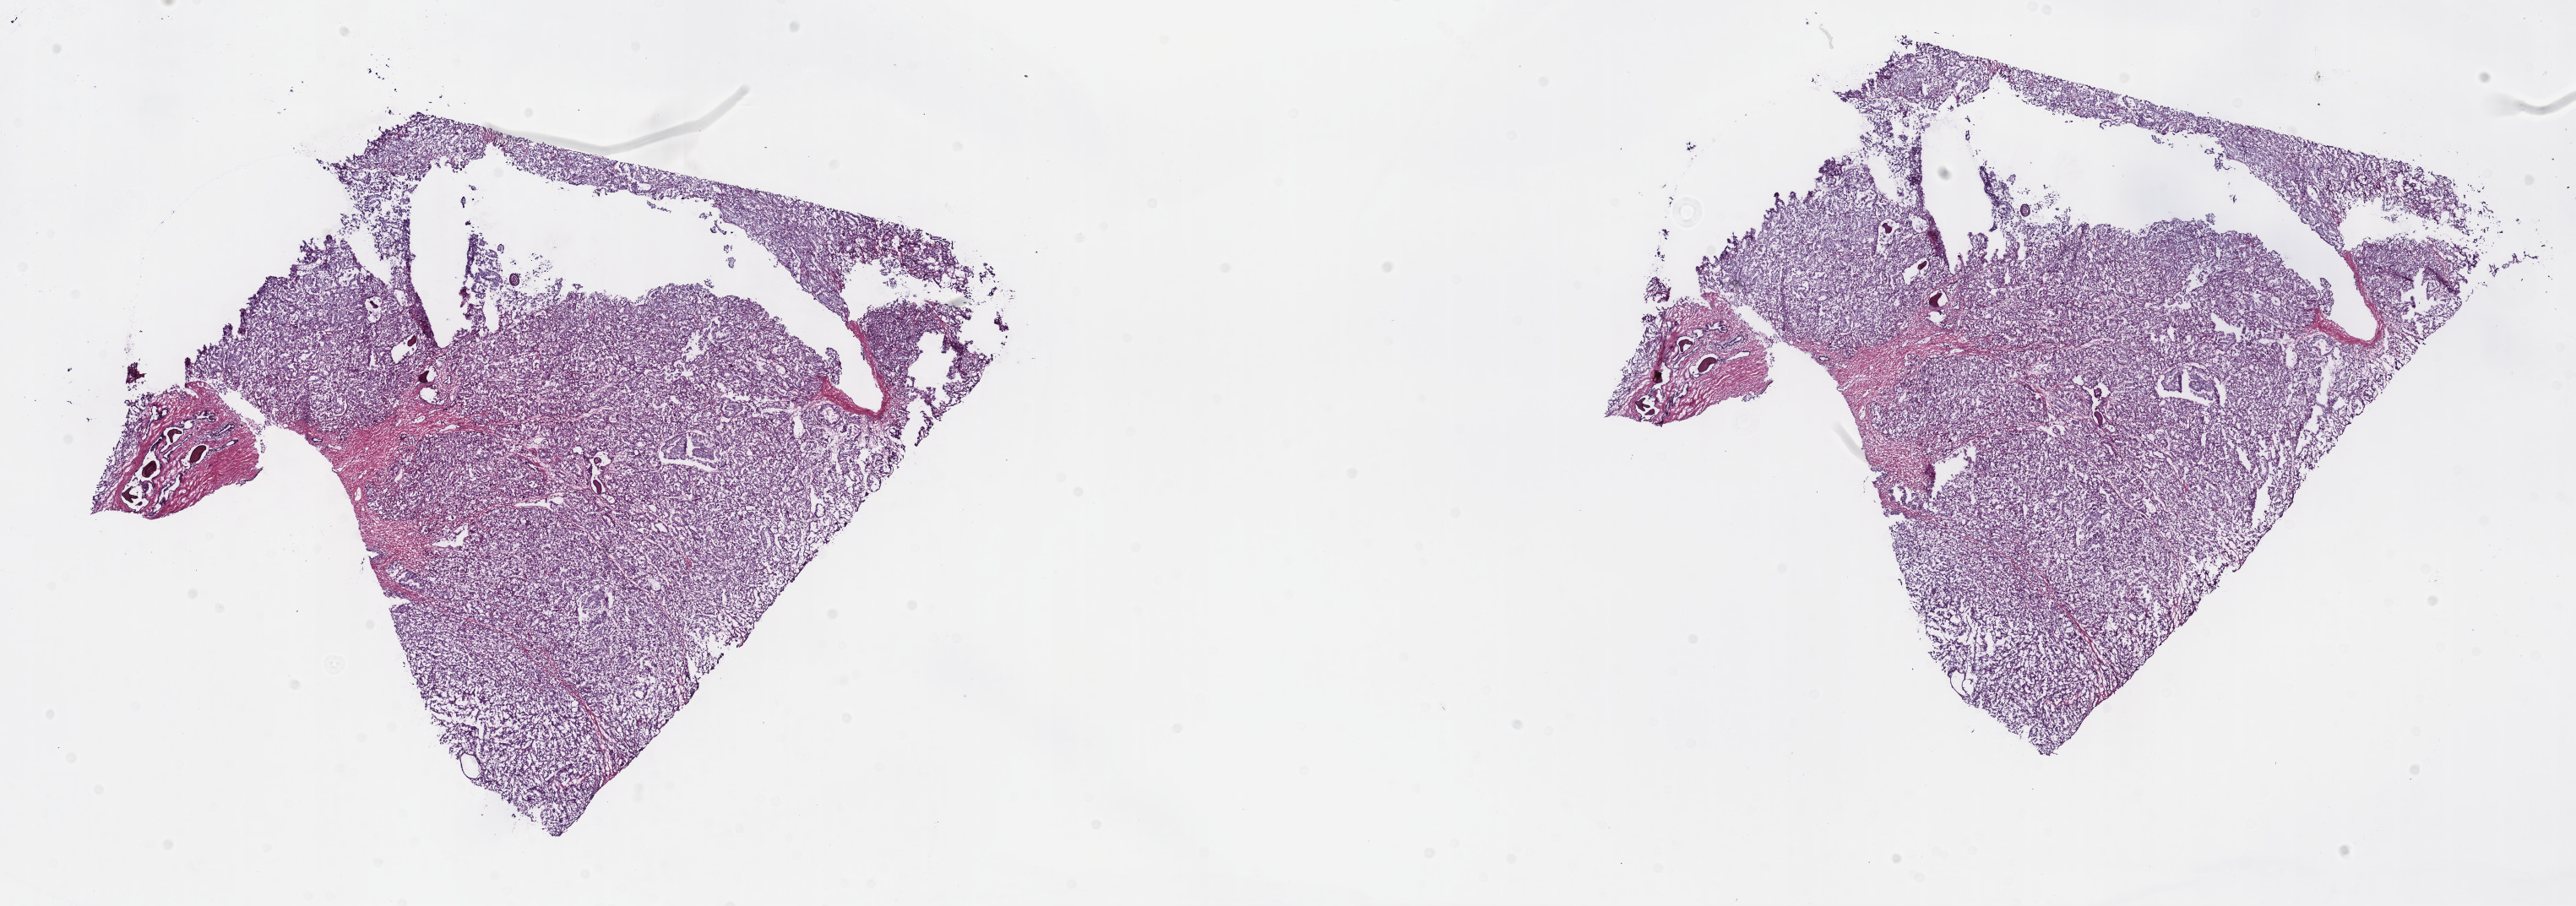
Whole-slide histology image, H&E-stained, a low-resolution overview of the entire scanned area, about 24.7 x 8.7 mm (acquisition: 40x scan), frozen section, sample: primary tumour, prostate. Patient: male, age at initial diagnosis 65 years. Gleason score: 6 (3+3). Composition of this section per pathologist review: tumour cells 85%, tumour nuclei 90%, normal cells 10%, stromal cells 5%, necrosis 0%. Inflammatory infiltration, as recorded: lymphocyte infiltration 0%, monocyte infiltration 0%, neutrophil infiltration 0%.
• lymph nodes positive (case pathology): 0 of 8 examined
• laterality: bilateral
• histologic diagnosis: Adenocarcinoma, NOS